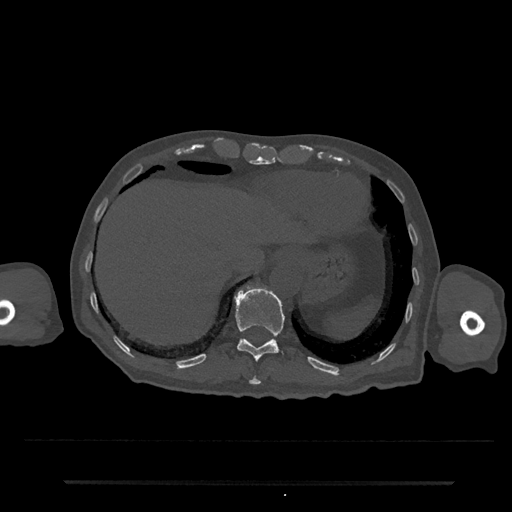
CT including the spine, one axial slice. Position 254 of 797 along the scan axis. Reconstruction kernel Br40s/3. 120 kVp. Bone window (W 1800 / L 400 HU). 0.5 mm slice thickness. 512 × 512 image matrix, field of view 427 × 427 mm. Patient: male, 74 years. From the clinical record (not read from this slice): primary cancer: prostate.
Annotated regions visible in this slice (semi-automatic segmentation, software-assisted and operator-edited):
- T10 vertebra: bounding box (x1, y1, x2, y2) in pixels: (249, 376, 261, 385)
- T11 vertebra: (234, 284, 285, 362)